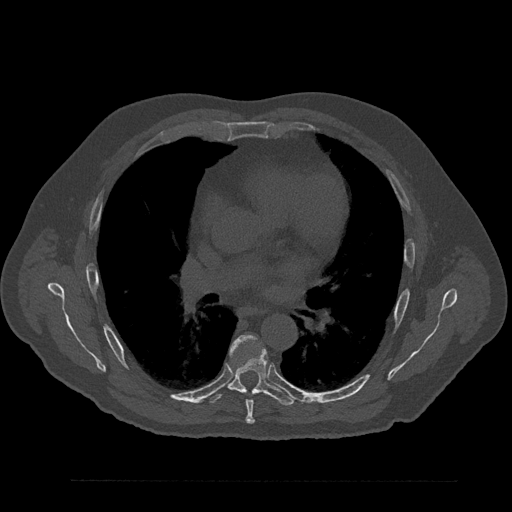
CT including the spine, one axial slice; slice 527 of 797 in the series (ordered by position); 120 kVp; bone window (W 1800 / L 400 HU); 0.5 mm slice thickness; 512 × 512 image matrix. Male patient, age 61 years. Case-level facts recorded for this patient, not image findings: primary cancer: prostate.
Structures marked on this image (semi-automatic segmentation, software-assisted and operator-edited):
- T6 vertebra: bounding box [x1, y1, x2, y2] px = [230, 336, 260, 424]
- T7 vertebra: [208, 345, 294, 406]